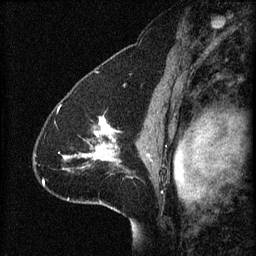
Breast MRI (dynamic contrast-enhanced), one sagittal slice. Position 44 of 60 along the scan axis. 3 images stored at this slice position (order not interpretable as contrast timing). 1.5 T. TE 4.2 ms, TR 8.2 ms. 2 mm slice thickness. 256 × 256 image matrix. Patient: female, 41 years.
Structures marked on this image (semi-automatically segmented with operator editing):
- analysis volume of interest (the breast-tissue region the enhancement analysis was run in; not a lesion): bounding box [x1, y1, x2, y2] px = [59, 110, 122, 171]
- tumour enhancement mask (voxels above the 70 % enhancement threshold inside the analysis volume of interest): [64, 116, 121, 169]